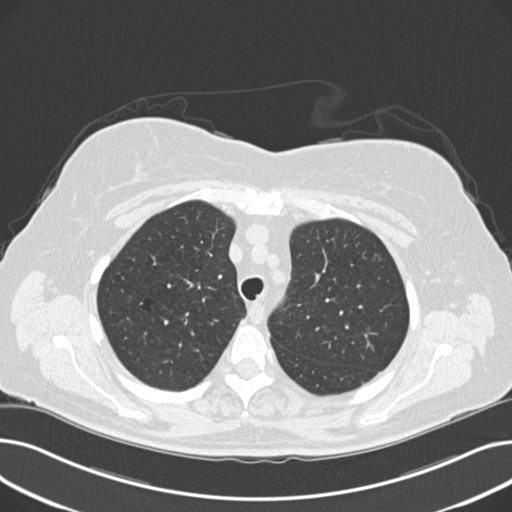
Low-dose screening chest CT, axial slice; third annual screen; lung window (W 1500 / L -600 HU); 2 mm slice thickness; standard (soft-tissue) reconstruction kernel (B30f); slice 53 of 203 in the series. Female participant, aged 60 years at enrolment. Current smoker at enrolment.
Expert-annotated lung lesion, bounding box <359,241,393,276> (left, top, right, bottom; pixels). The screening reader recorded 8 non-calcified nodules or masses ≥4 mm on this exam (right upper lobe, lingula, lingula, right middle lobe, right lower lobe, left lower lobe, left lower lobe, left lower lobe); which of them this box marks is not recorded. Official screen result: positive, other. Later outcome: lung cancer diagnosed 176 days after this screen — non-small cell carcinoma, left upper lobe, poorly differentiated (G3), stage IB (AJCC 6th edition), 7 mm at pathology.